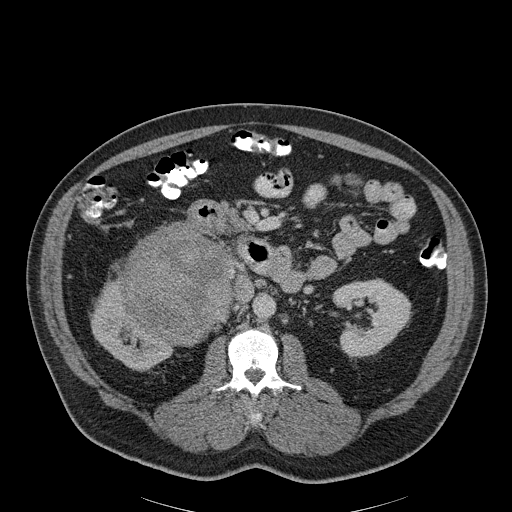
Contrast-enhanced abdominal CT, one axial slice. Position 110 of 186 along the scan axis. 120 kVp. Soft-tissue window (W 400 / L 40 HU). 3 mm slice thickness. 512 × 512 image matrix, field of view 464 × 464 mm. Male patient, age 56 years. Case-level facts recorded for this patient, not image findings: diagnosis: adrenocortical carcinoma; tumour side: right adrenal.
Outlined on this slice (semi-automatic segmentation, software-assisted and operator-edited):
- mass: bounding box [x1, y1, x2, y2] px = [123, 225, 232, 342]